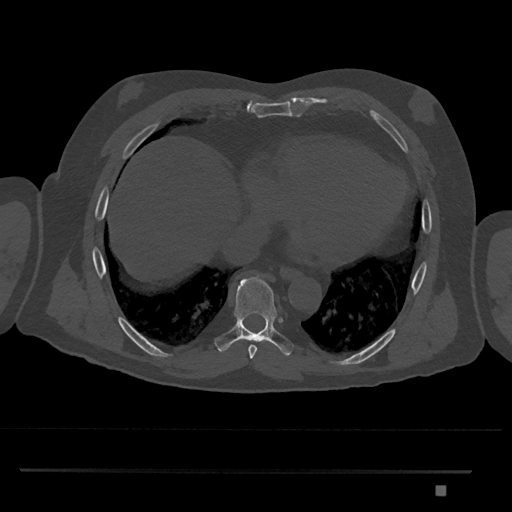
CT including the spine, one axial slice; slice 1119 of 1134 in the series (ordered by position); reconstruction kernel Br40s/3; 120 kVp; bone window (W 1800 / L 400 HU); 512 × 512 image matrix, field of view 429 × 429 mm. Male patient, age 65 years. Case-level facts recorded for this patient, not image findings: primary cancer: prostate.
Annotated regions visible in this slice (semi-automatically segmented with operator editing):
- T8 vertebra: bounding box [x1, y1, x2, y2] px = [214, 275, 294, 356]